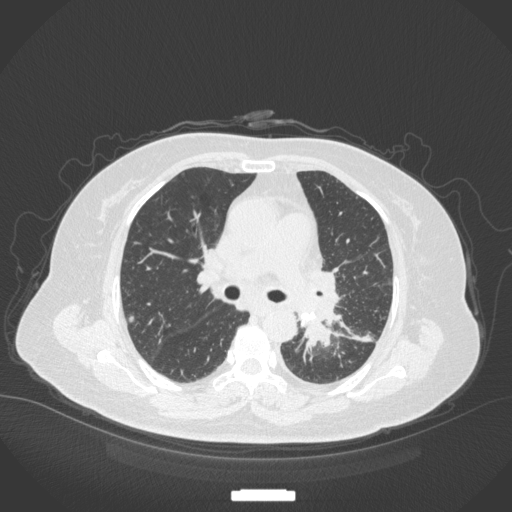
Chest CT, one axial slice. Position 211 of 328 along the scan axis. Reconstruction kernel B31f. 120 kVp. Lung window (W 1500 / L -600 HU). 512 × 512 image matrix, field of view 400 × 400 mm. Female patient, age 69 years. Case-level facts recorded for this patient, not image findings: clinical TNM (as recorded): T2b N3 M1.
Outlined on this slice (bounding box drawn by a radiologist):
- lung tumour (recorded histology: adenocarcinoma): box from (x=296, y=304) to (x=332, y=368) px